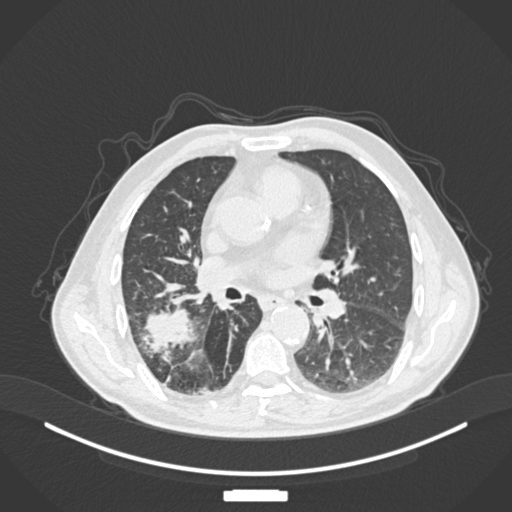
Chest CT, one axial slice; slice 86 of 201 in the series (ordered by position); reconstruction kernel B30f; lung window (W 1500 / L -600 HU); 512 × 512 image matrix, field of view 400 × 400 mm. Male patient, age 72 years. Case-level facts recorded for this patient, not image findings: clinical TNM (as recorded): T3 N2 M0.
Outlined on this slice (rectangle marked by the reading radiologist):
- lung tumour (recorded histology: adenocarcinoma): bounding box <134,302,195,358> (left, top, right, bottom; pixels)